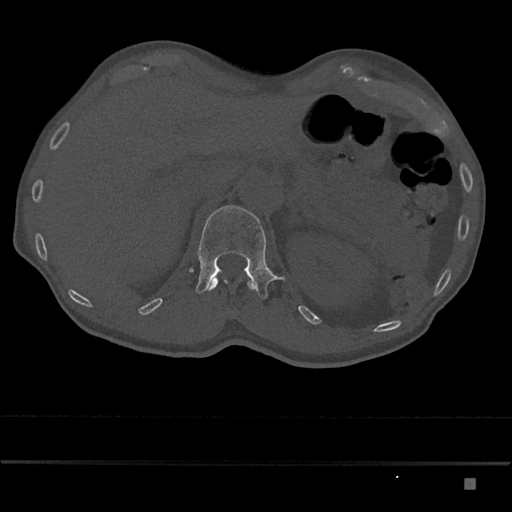
CT including the spine, one axial slice. Slice 566 of 797 in the series (ordered by position). Reconstruction kernel Br40s/3. Bone window (W 1800 / L 400 HU). 512 × 512 image matrix. Patient: male, 72 years. Case-level facts recorded for this patient, not image findings: primary cancer: prostate.
Structures marked on this image (semi-automatically segmented with operator editing):
- L1 vertebra: bounding box (x1, y1, x2, y2) in pixels: (196, 205, 286, 299)
- T12 vertebra: (206, 276, 258, 291)